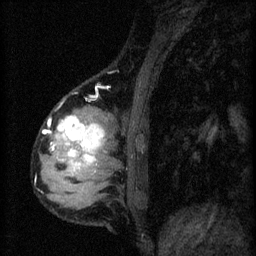
Breast MRI (dynamic contrast-enhanced), one sagittal slice. Slice 15 of 60 in the series (ordered by position). 3 images stored at this slice position (order not interpretable as contrast timing). 1.5 T. TE 4.2 ms, TR 8.2 ms. 2 mm slice thickness. 256 × 256 image matrix, field of view 180 × 180 mm. Female patient, age 37 years.
Outlined on this slice (semi-automatically segmented with operator editing):
- analysis volume of interest (the breast-tissue region the enhancement analysis was run in; not a lesion): box from (x=44, y=102) to (x=119, y=197) px
- tumour enhancement mask (voxels above the 70 % enhancement threshold inside the analysis volume of interest): (x=48, y=116)–(x=106, y=169)